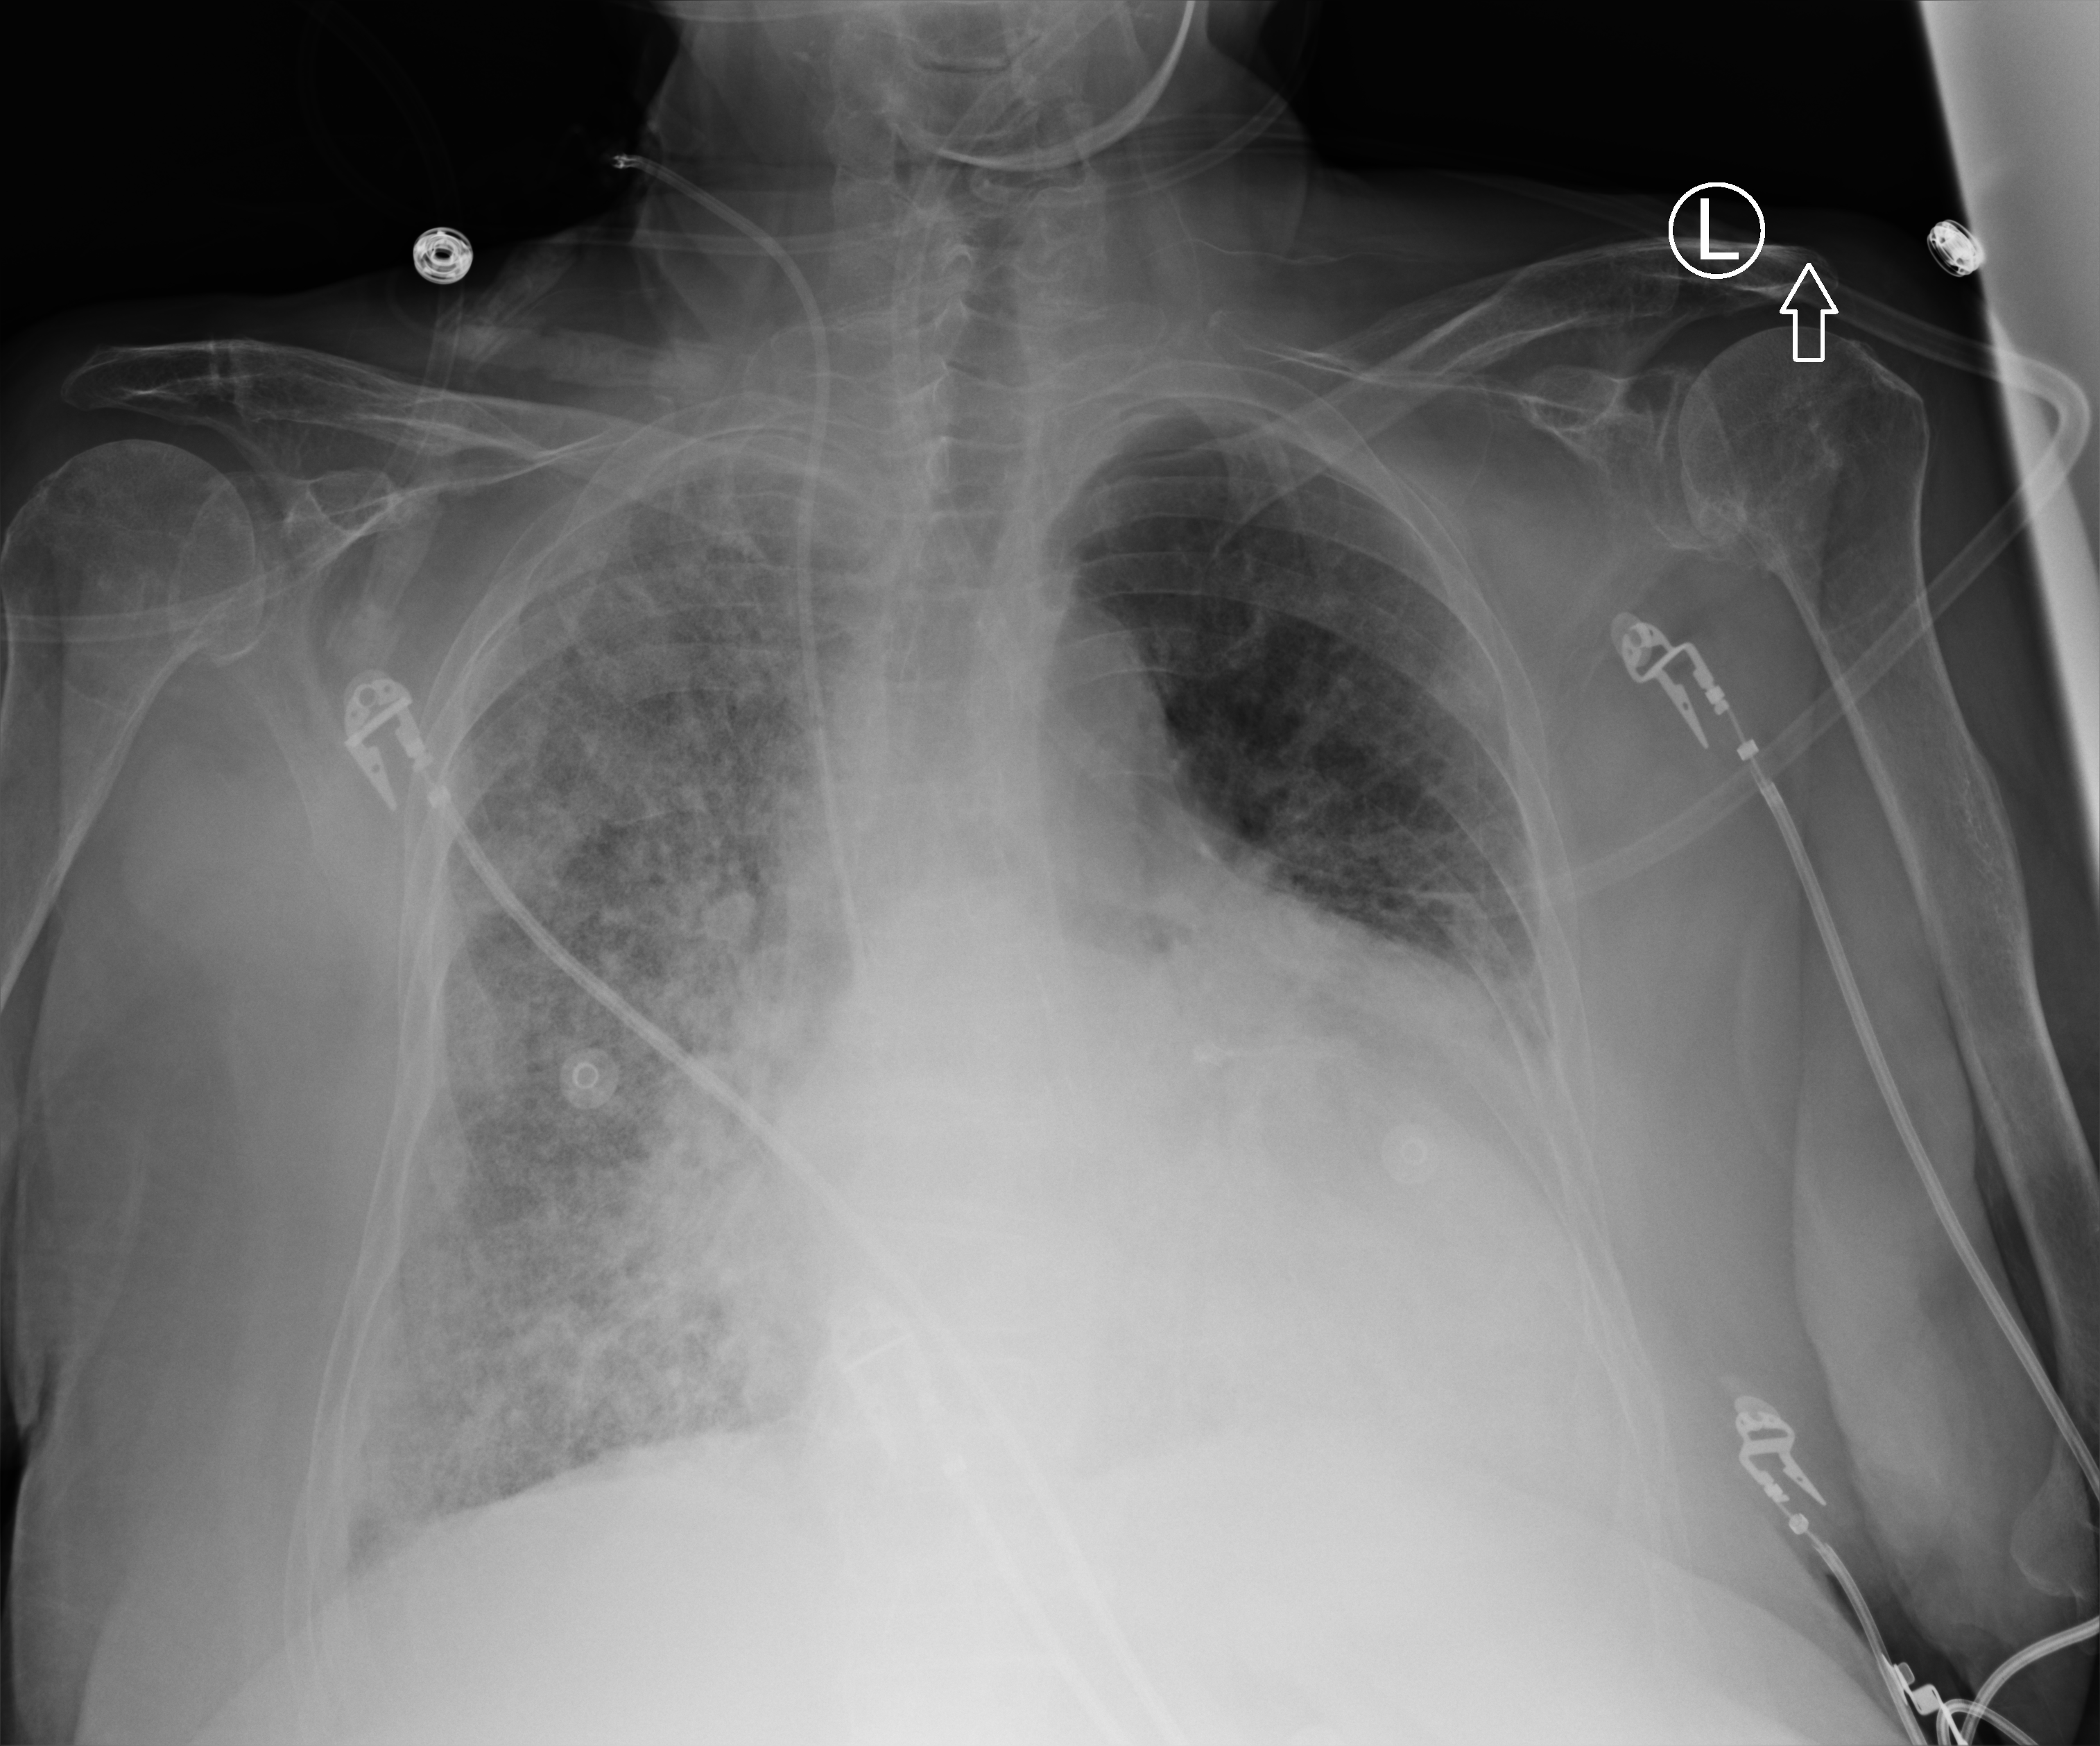
Portable chest radiograph; anteroposterior (AP) projection. Patient hospitalised with COVID-19; female, aged 75–90 years.
Hospital-stay facts (about this admission, not read from this image; timing relative to this image not recorded): mechanically ventilated during this hospital stay: no.